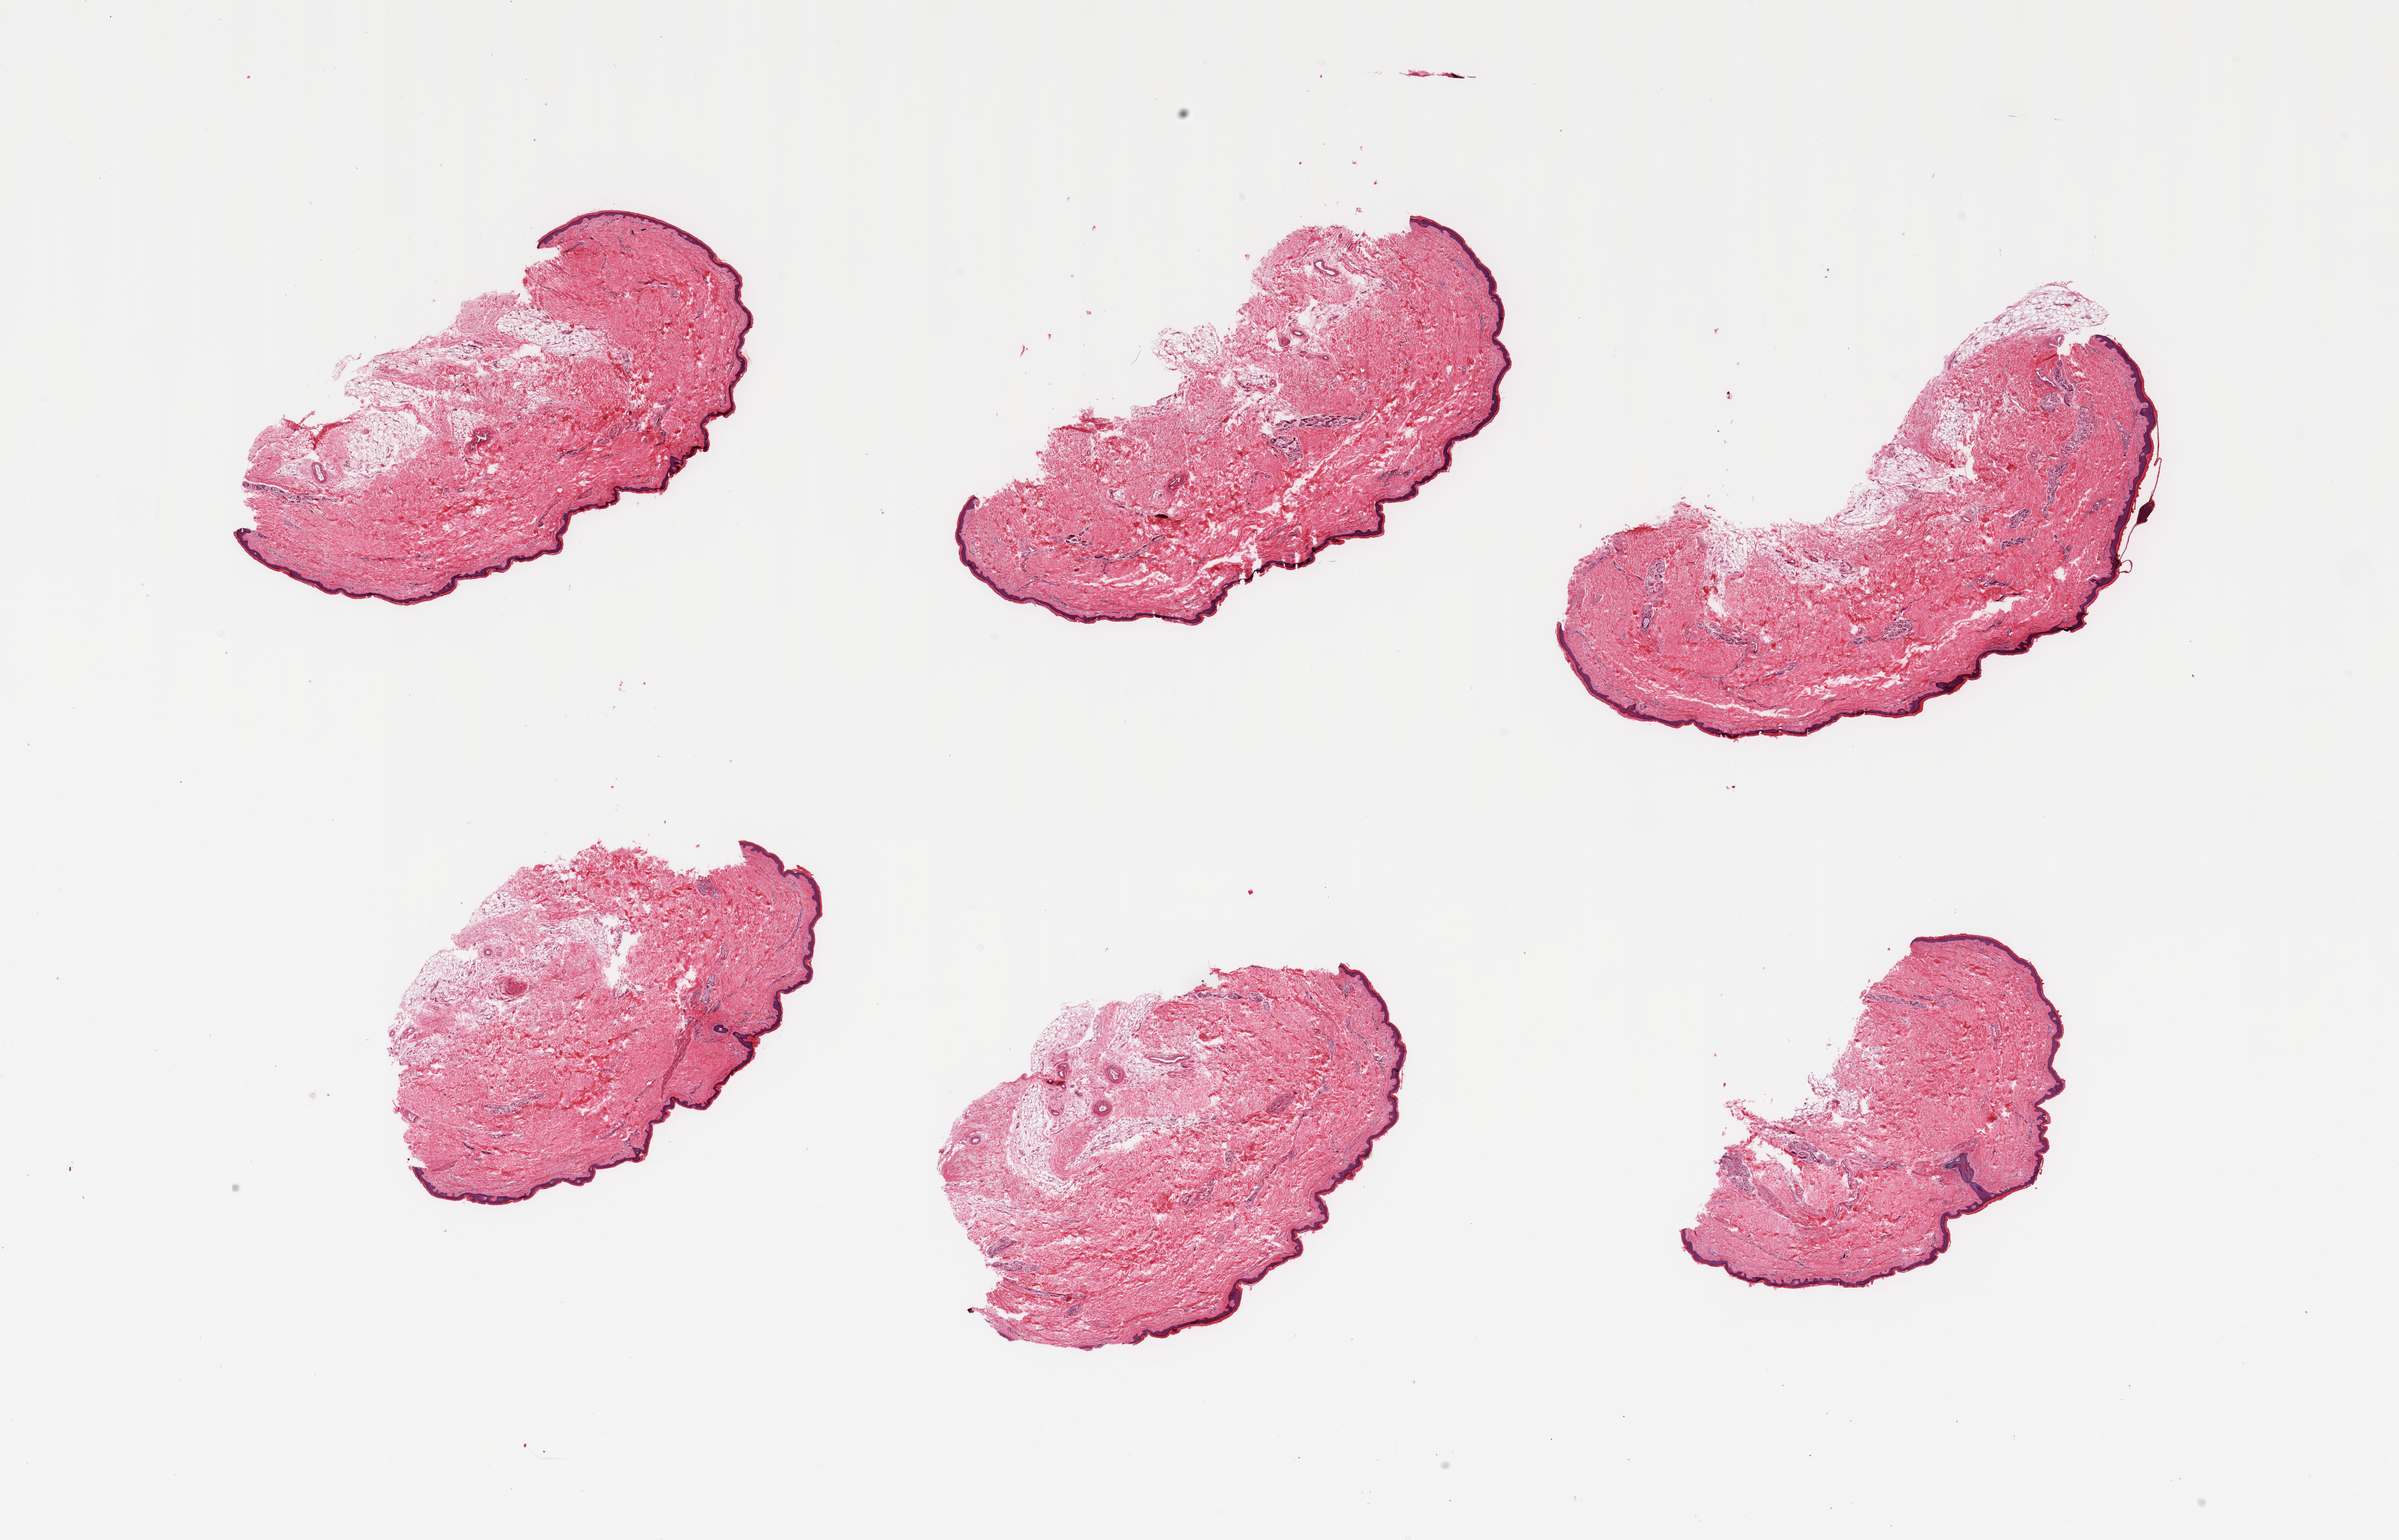
Whole-slide image, hematoxylin and eosin (H&E) stain, brightfield, a low-resolution overview of the entire scanned area, about 30.5 x 19.6 mm (slide scanned at 20x). PAXgene-fixed, paraffin-embedded tissue. Sampled site (target tissue): skin of lower leg. Tissue donor sample. Male donor.
• reviewer comment on this tissue sample: 6 pieces; few pieces with up to 10% internal/external fat, epidermis measures 46 microns